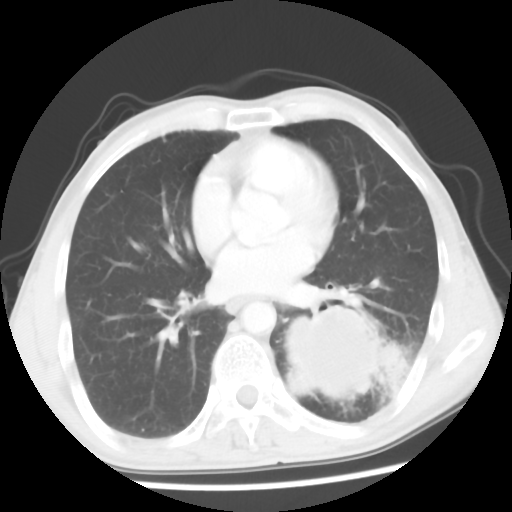
Chest CT, one axial slice. Slice 26 of 56 in the series (ordered by position). 120 kVp. Lung window (W 1500 / L -600 HU). 512 × 512 image matrix, field of view 318 × 318 mm. Male patient, age 60 years. Case-level facts recorded for this patient, not image findings: clinical TNM (as recorded): T4 N0 M0.
Structures marked on this image (rectangle marked by the reading radiologist):
- lung tumour (recorded histology: squamous cell carcinoma): bounding box [x1, y1, x2, y2] px = [278, 295, 385, 407]